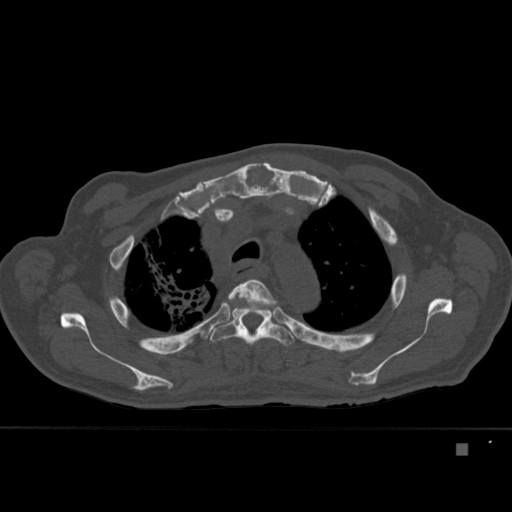
CT including the spine, one axial slice. Position 326 of 451 along the scan axis. Bone window (W 1800 / L 400 HU). 512 × 512 image matrix, field of view 378 × 378 mm. Patient: male, 75 years. Case-level facts recorded for this patient, not image findings: primary cancer: prostate.
Structures marked on this image (semi-automatically segmented with operator editing):
- T3 vertebra: bounding box (x1, y1, x2, y2) in pixels: (223, 279, 277, 316)
- T4 vertebra: (208, 305, 295, 346)